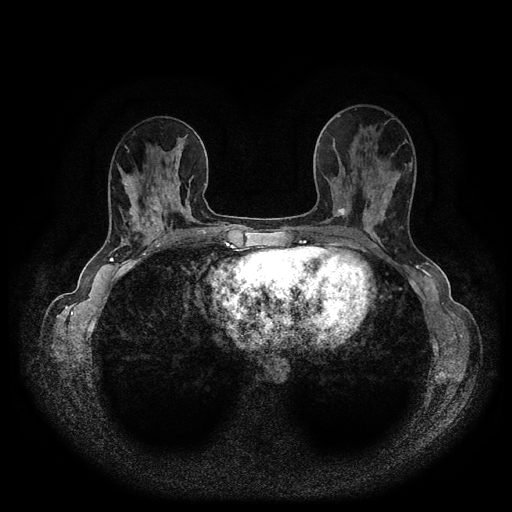
Breast MRI (dynamic contrast-enhanced, multi-phase), one axial slice. Slice 39 of 116 in the series (ordered by position). Dynamic contrast-enhanced series, time point 2 of 5 at this slice position (early post-contrast). 1.5 T. TE 2.6 ms, TR 5.4 ms. 512 × 512 image matrix, field of view 340 × 340 mm. Female patient, age 40 years.
Annotated regions visible in this slice (semi-automatically segmented with operator editing):
- breast lesion (labelled 'tumour' in the annotation; benign lesions carry a separate 'benign' label): box from (x=334, y=207) to (x=349, y=218) px